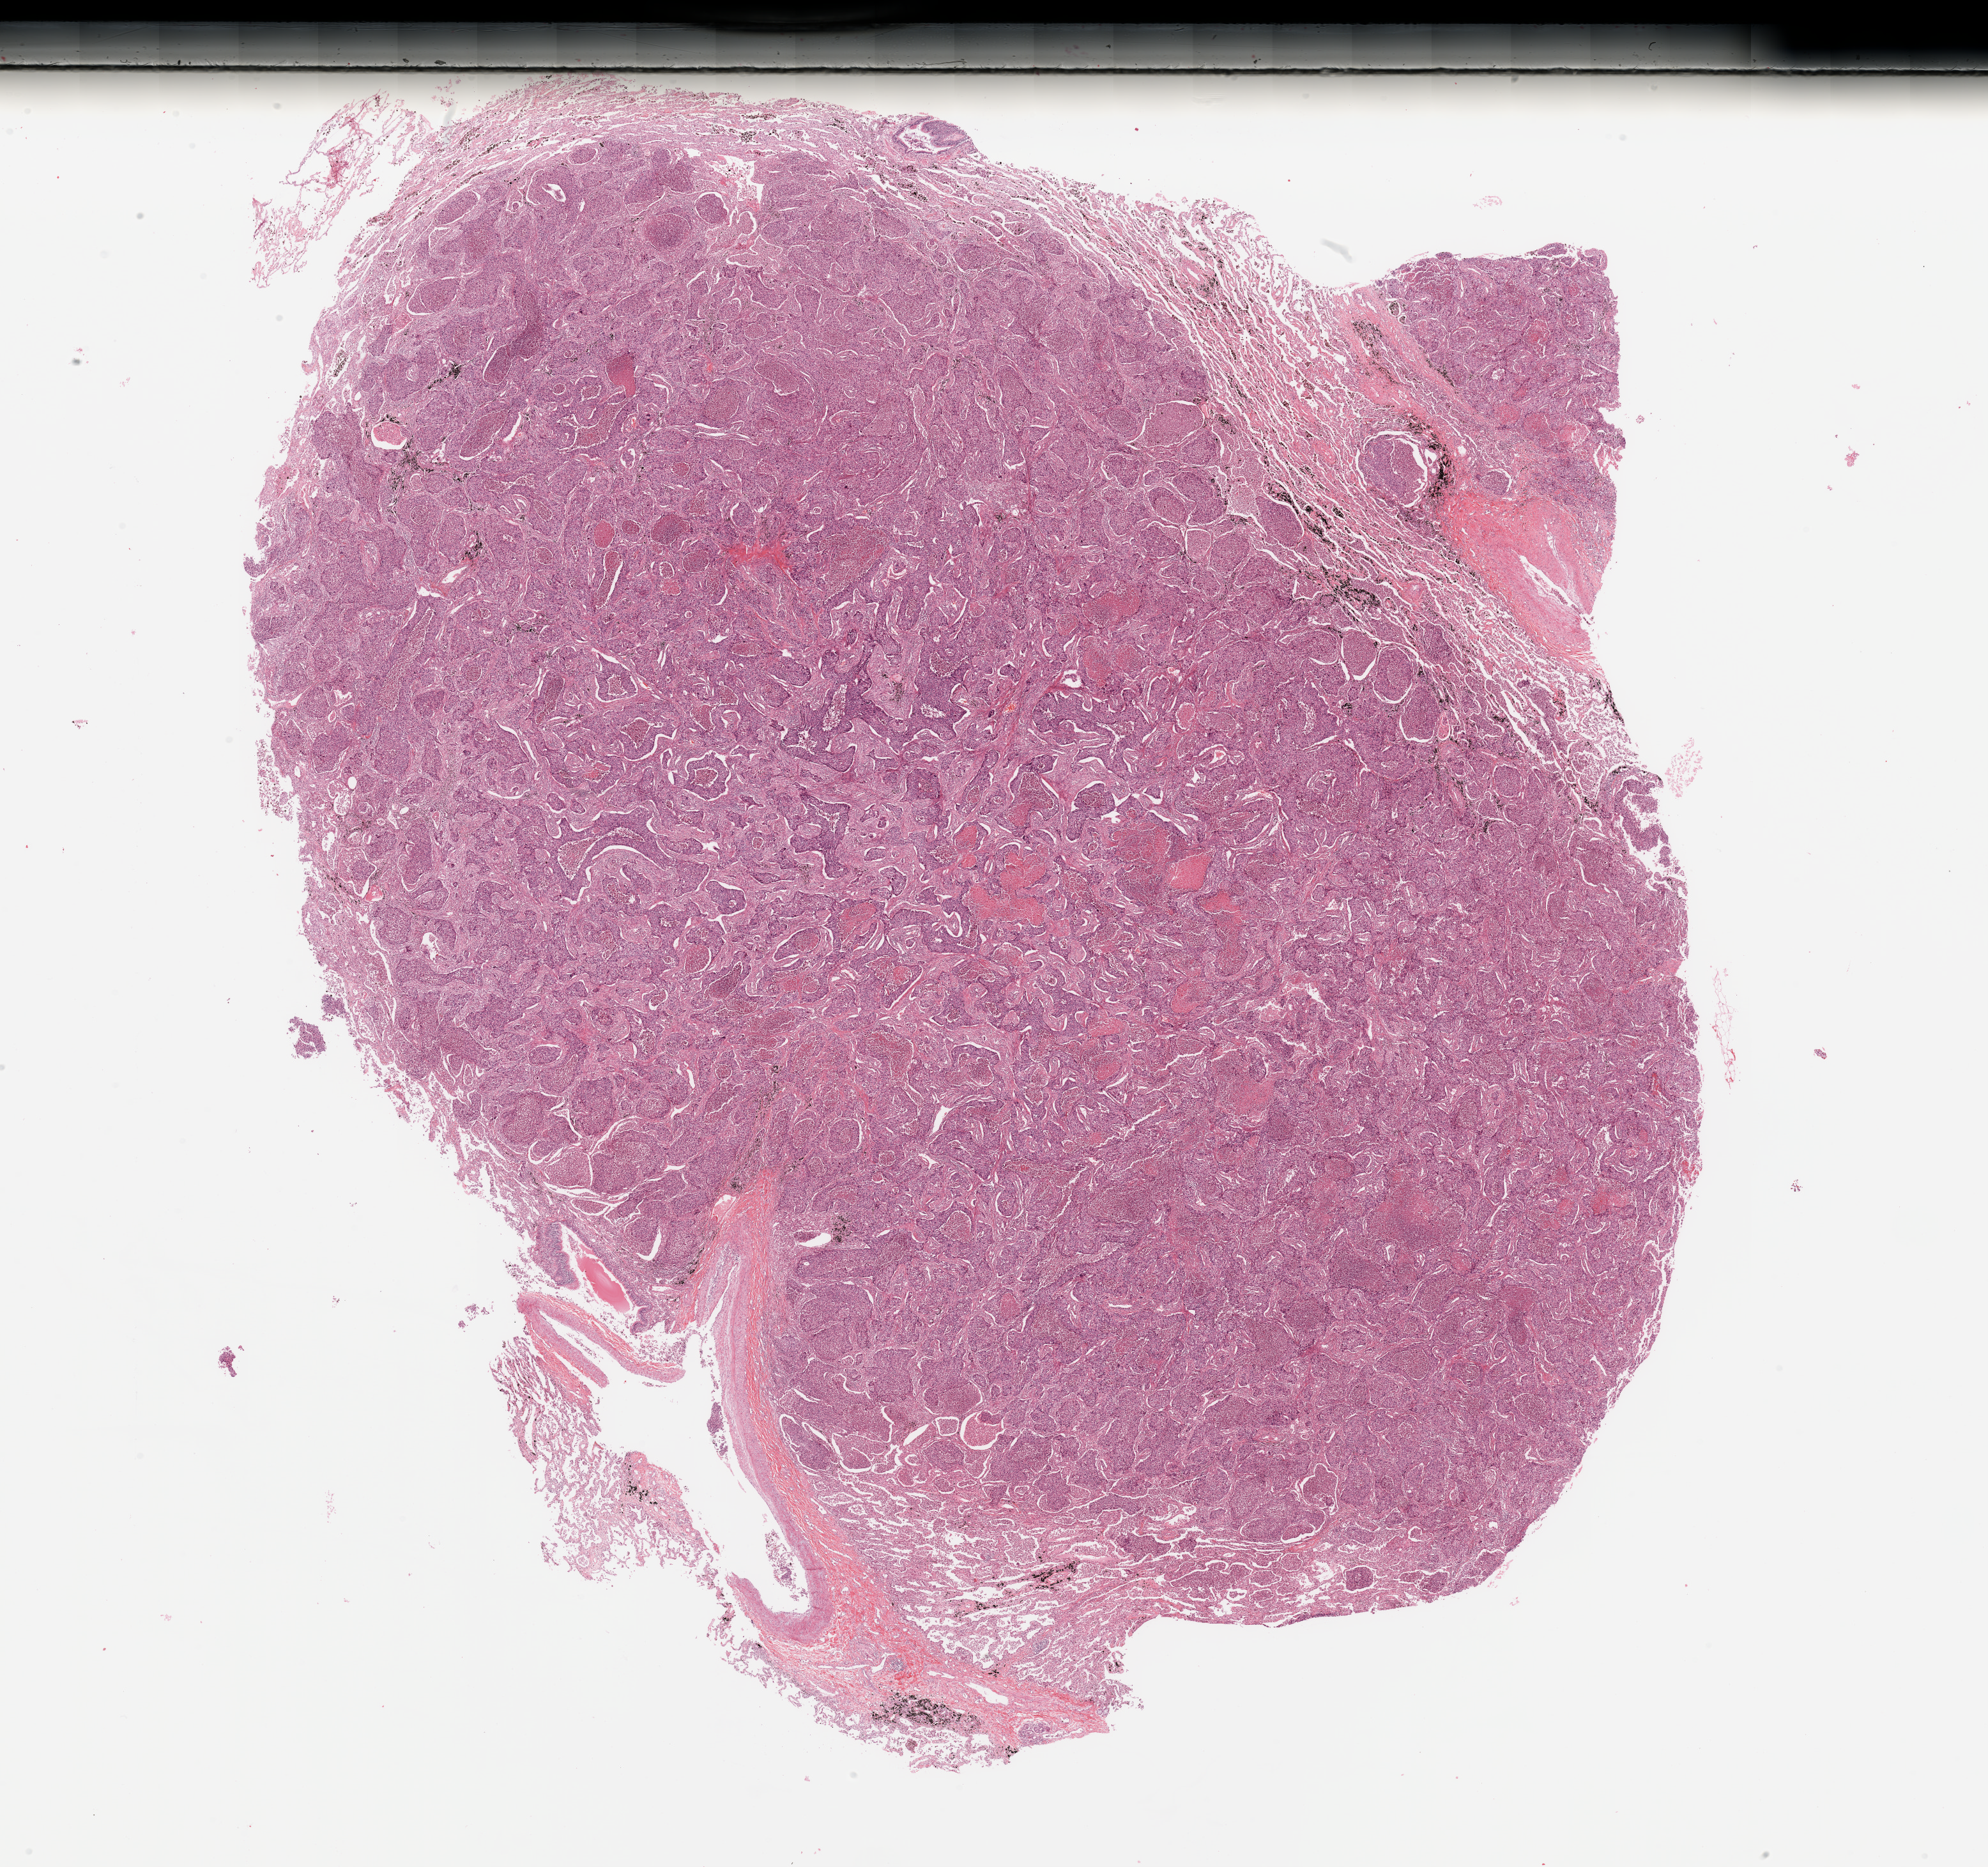
Digitized Hematoxylin and eosin (H&E) stained tissue section (whole slide) — a low-resolution overview of the entire scanned area, about 24.6 x 23.1 mm; tumour tissue sample, lung. Male, 65 y/o. Histologic grade: G3 (poorly differentiated).
Diagnosis: Squamous cell carcinoma, NOS. AJCC pathologic stage: IB.